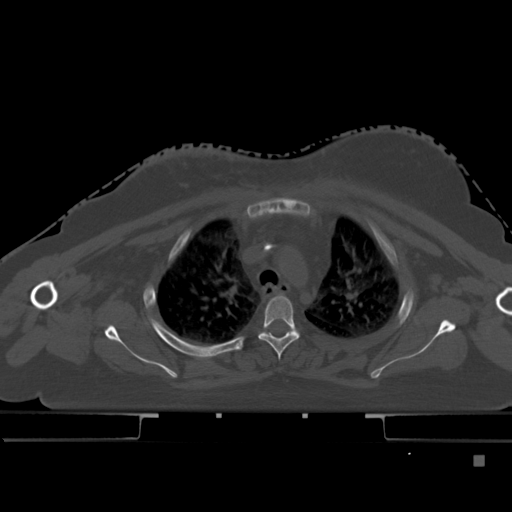
CT including the spine, one axial slice; slice 345 of 495 in the series (ordered by position); bone window (W 1800 / L 400 HU); 1.5 mm slice thickness; 512 × 512 image matrix, field of view 404 × 404 mm. Patient: female, 33 years. From the clinical record (not read from this slice): primary cancer: breast; vertebrae with lytic lesions (as recorded): T1.
Structures marked on this image (semi-automatically segmented with operator editing):
- T3 vertebra: box from (x=259, y=295) to (x=300, y=361) px